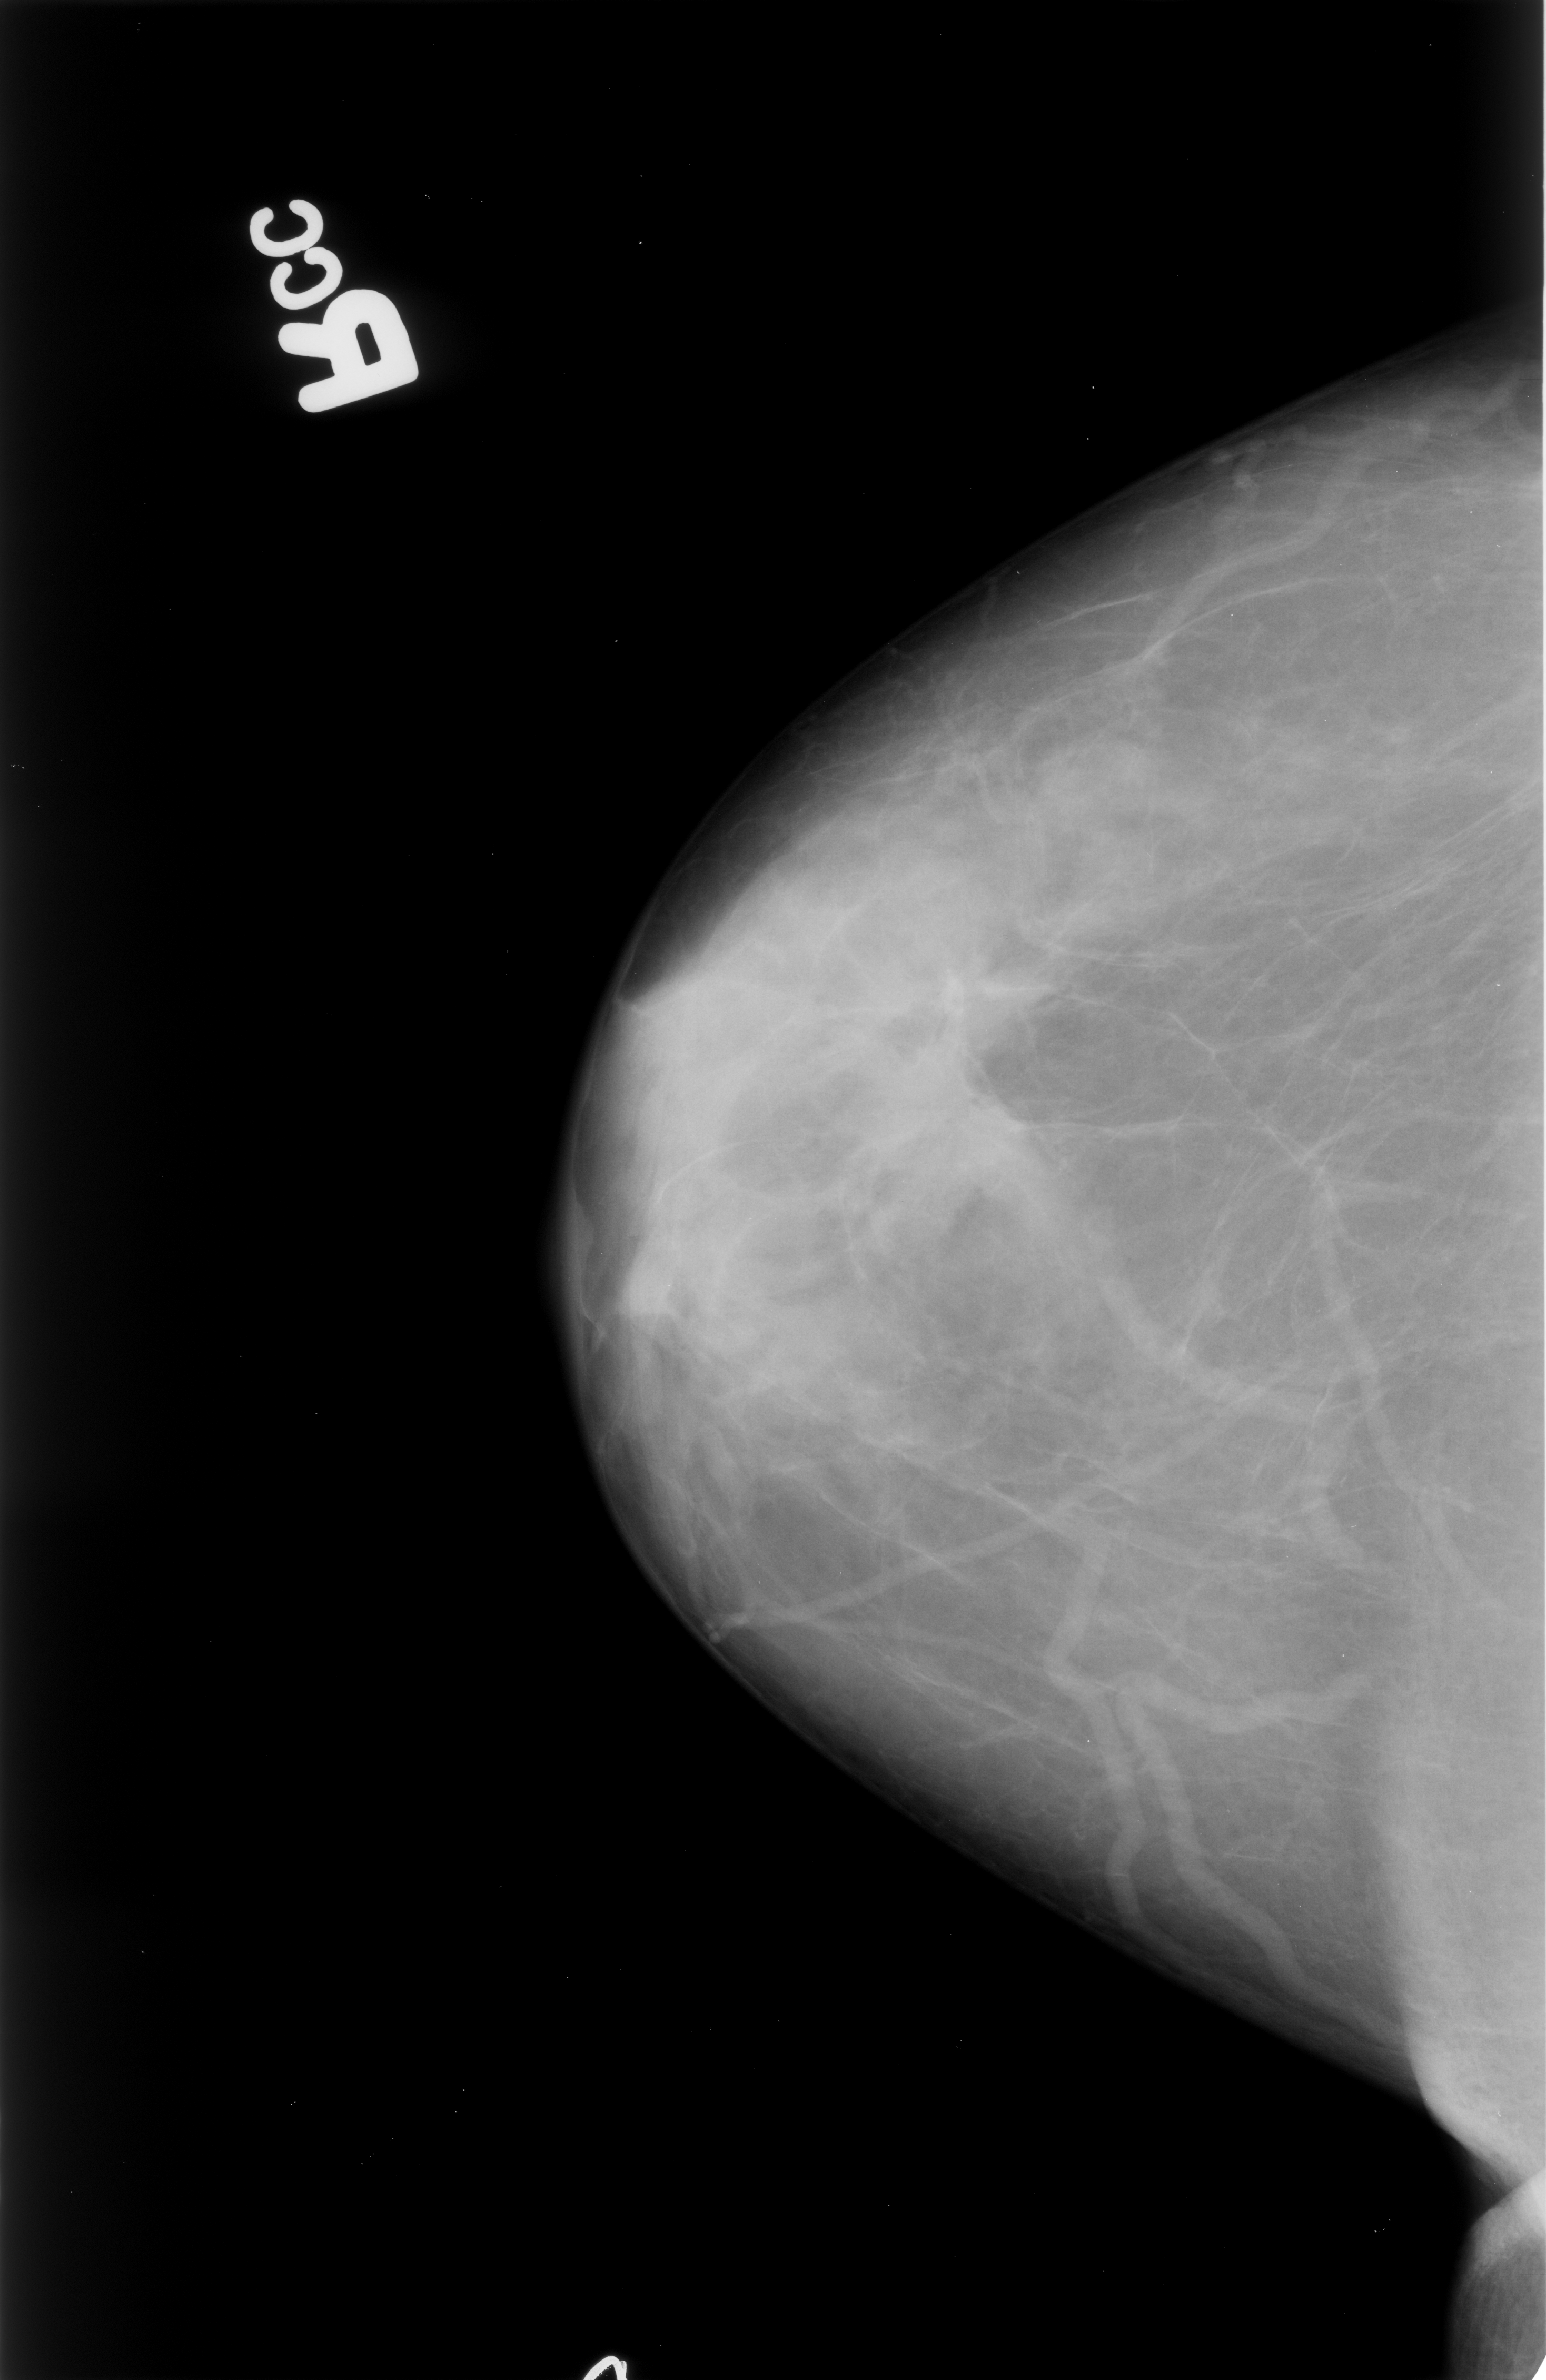
Mammogram (digitized film); right breast; CC view; breast composition: heterogeneously dense (BI-RADS density category 3 of 4).
Radiologist-marked abnormalities on this image: mass, shape irregular / architectural distortion, margins spiculated; BI-RADS assessment category 4; pathology (as recorded): malignant.